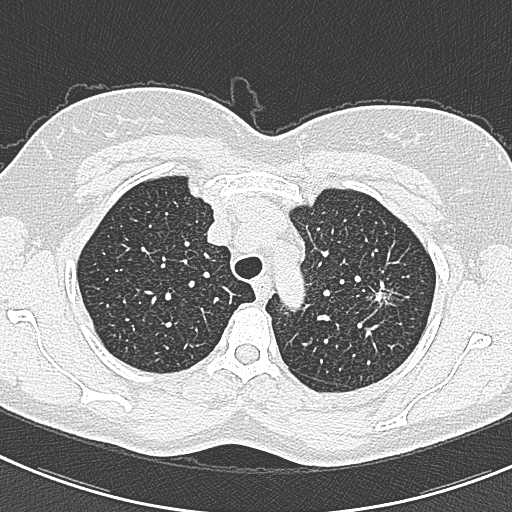
Low-dose screening chest CT, axial slice; baseline annual screen; lung window (W 1500 / L -600 HU); 120 kVp; slice 61 of 309 in the series. Female participant, aged 57 years at enrolment. Current smoker at enrolment.
Lesion marked by an expert reader, bounding box [x1, y1, x2, y2] px = [363, 275, 412, 321]. The screening reader recorded 2 non-calcified nodules or masses ≥4 mm on this exam; which of them this box marks is not recorded.